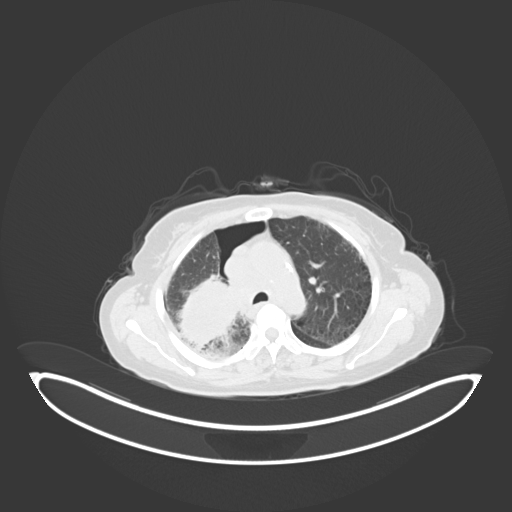
Chest CT, one axial slice; slice 42 of 69 in the series (ordered by position); reconstruction kernel B30f; 120 kVp; lung window (W 1500 / L -600 HU); 512 × 512 image matrix, field of view 500 × 500 mm. Patient: female, 64 years. Case-level facts recorded for this patient, not image findings: clinical TNM (as recorded): T3 N3 M0.
Structures marked on this image (bounding box drawn by a radiologist):
- lung tumour (recorded histology: squamous cell carcinoma): bounding box [x1, y1, x2, y2] px = [171, 275, 240, 354]